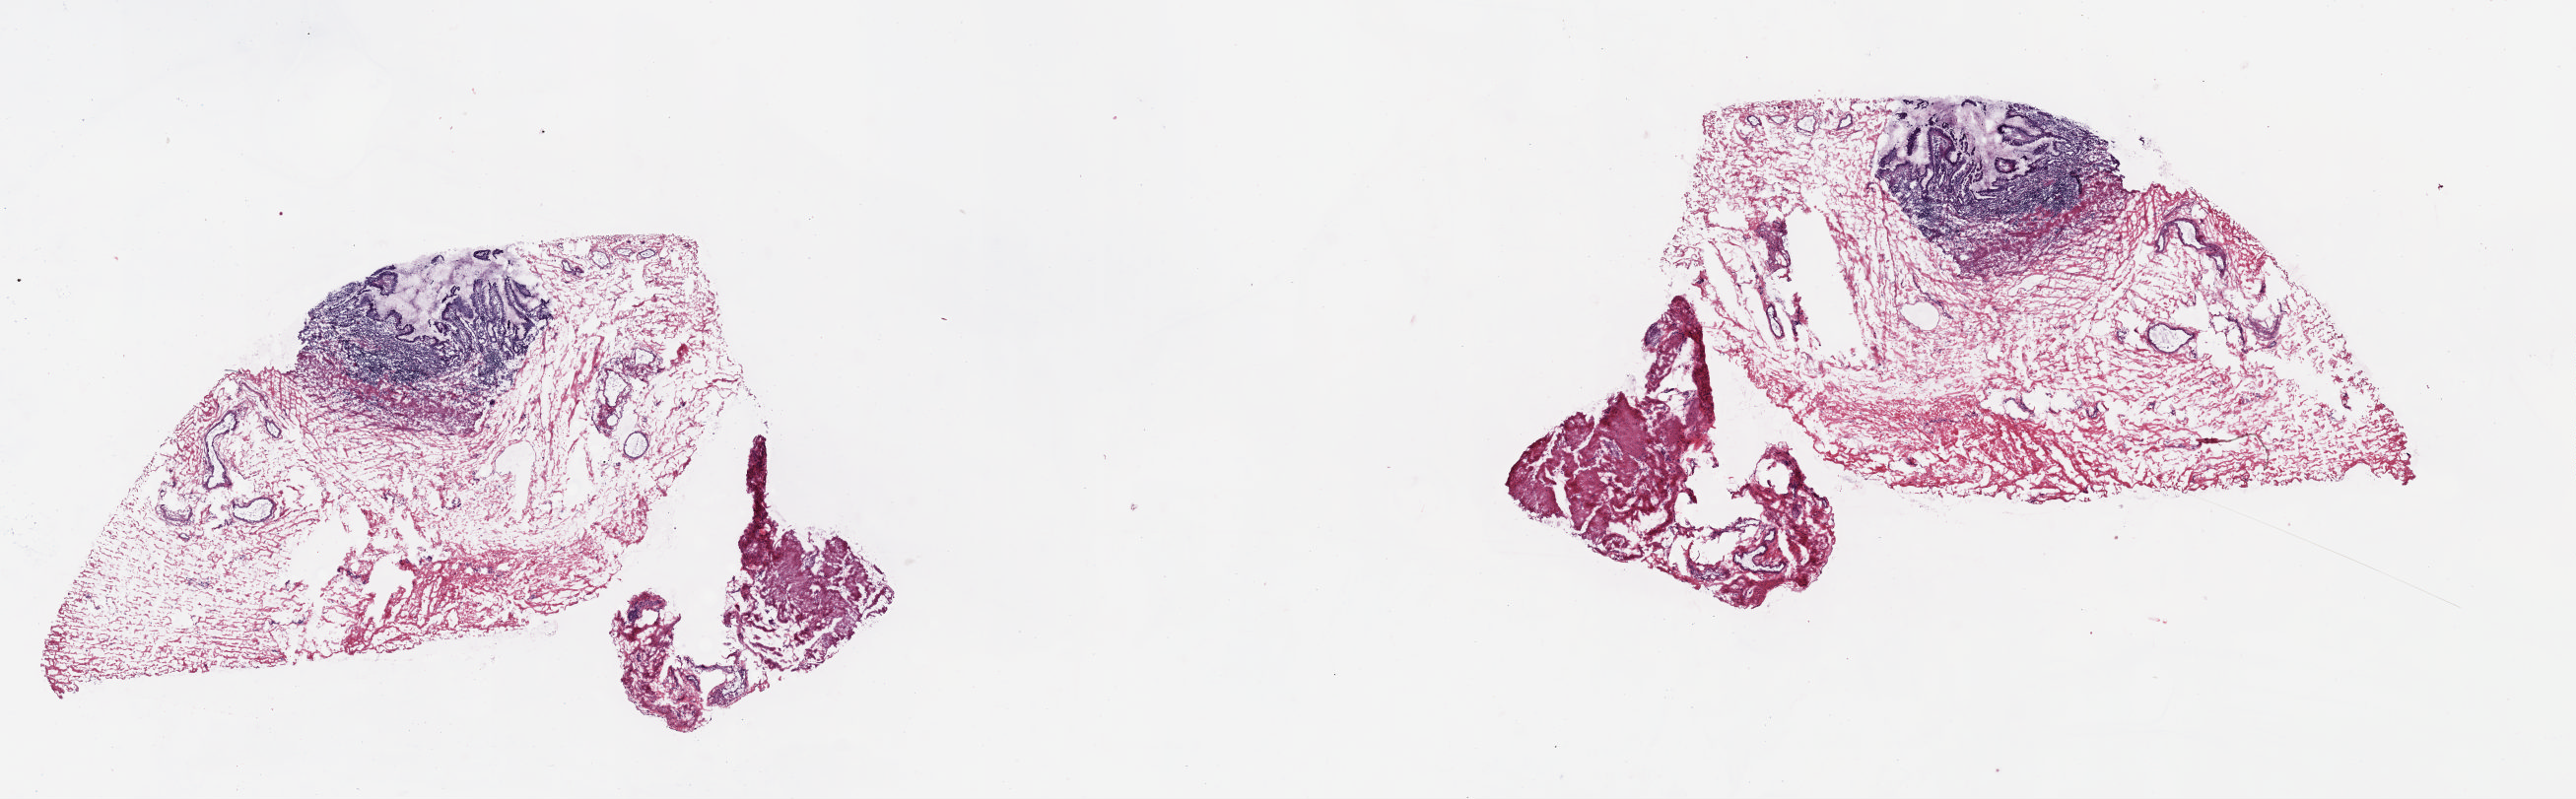
Digitized H&E-stained tissue section (whole slide) — a low-resolution overview of the entire scanned area, about 20.6 x 6.4 mm (slide scanned at 20x). Frozen section from the top of the tissue portion. Sample: solid tissue normal (non-tumour tissue), stomach. Patient: female, age at initial diagnosis 62 years. Slide review estimates, as recorded: tumour cells 0%, tumour nuclei 0%, normal cells 15%, stromal cells 85%, necrosis 0%. Inflammatory infiltration, as recorded: lymphocyte infiltration 0%, monocyte infiltration 0%, neutrophil infiltration 0%.
This section: solid tissue normal (non-tumour) sample from the same patient. Patient diagnosis: Carcinoma, diffuse type (gastric antrum).